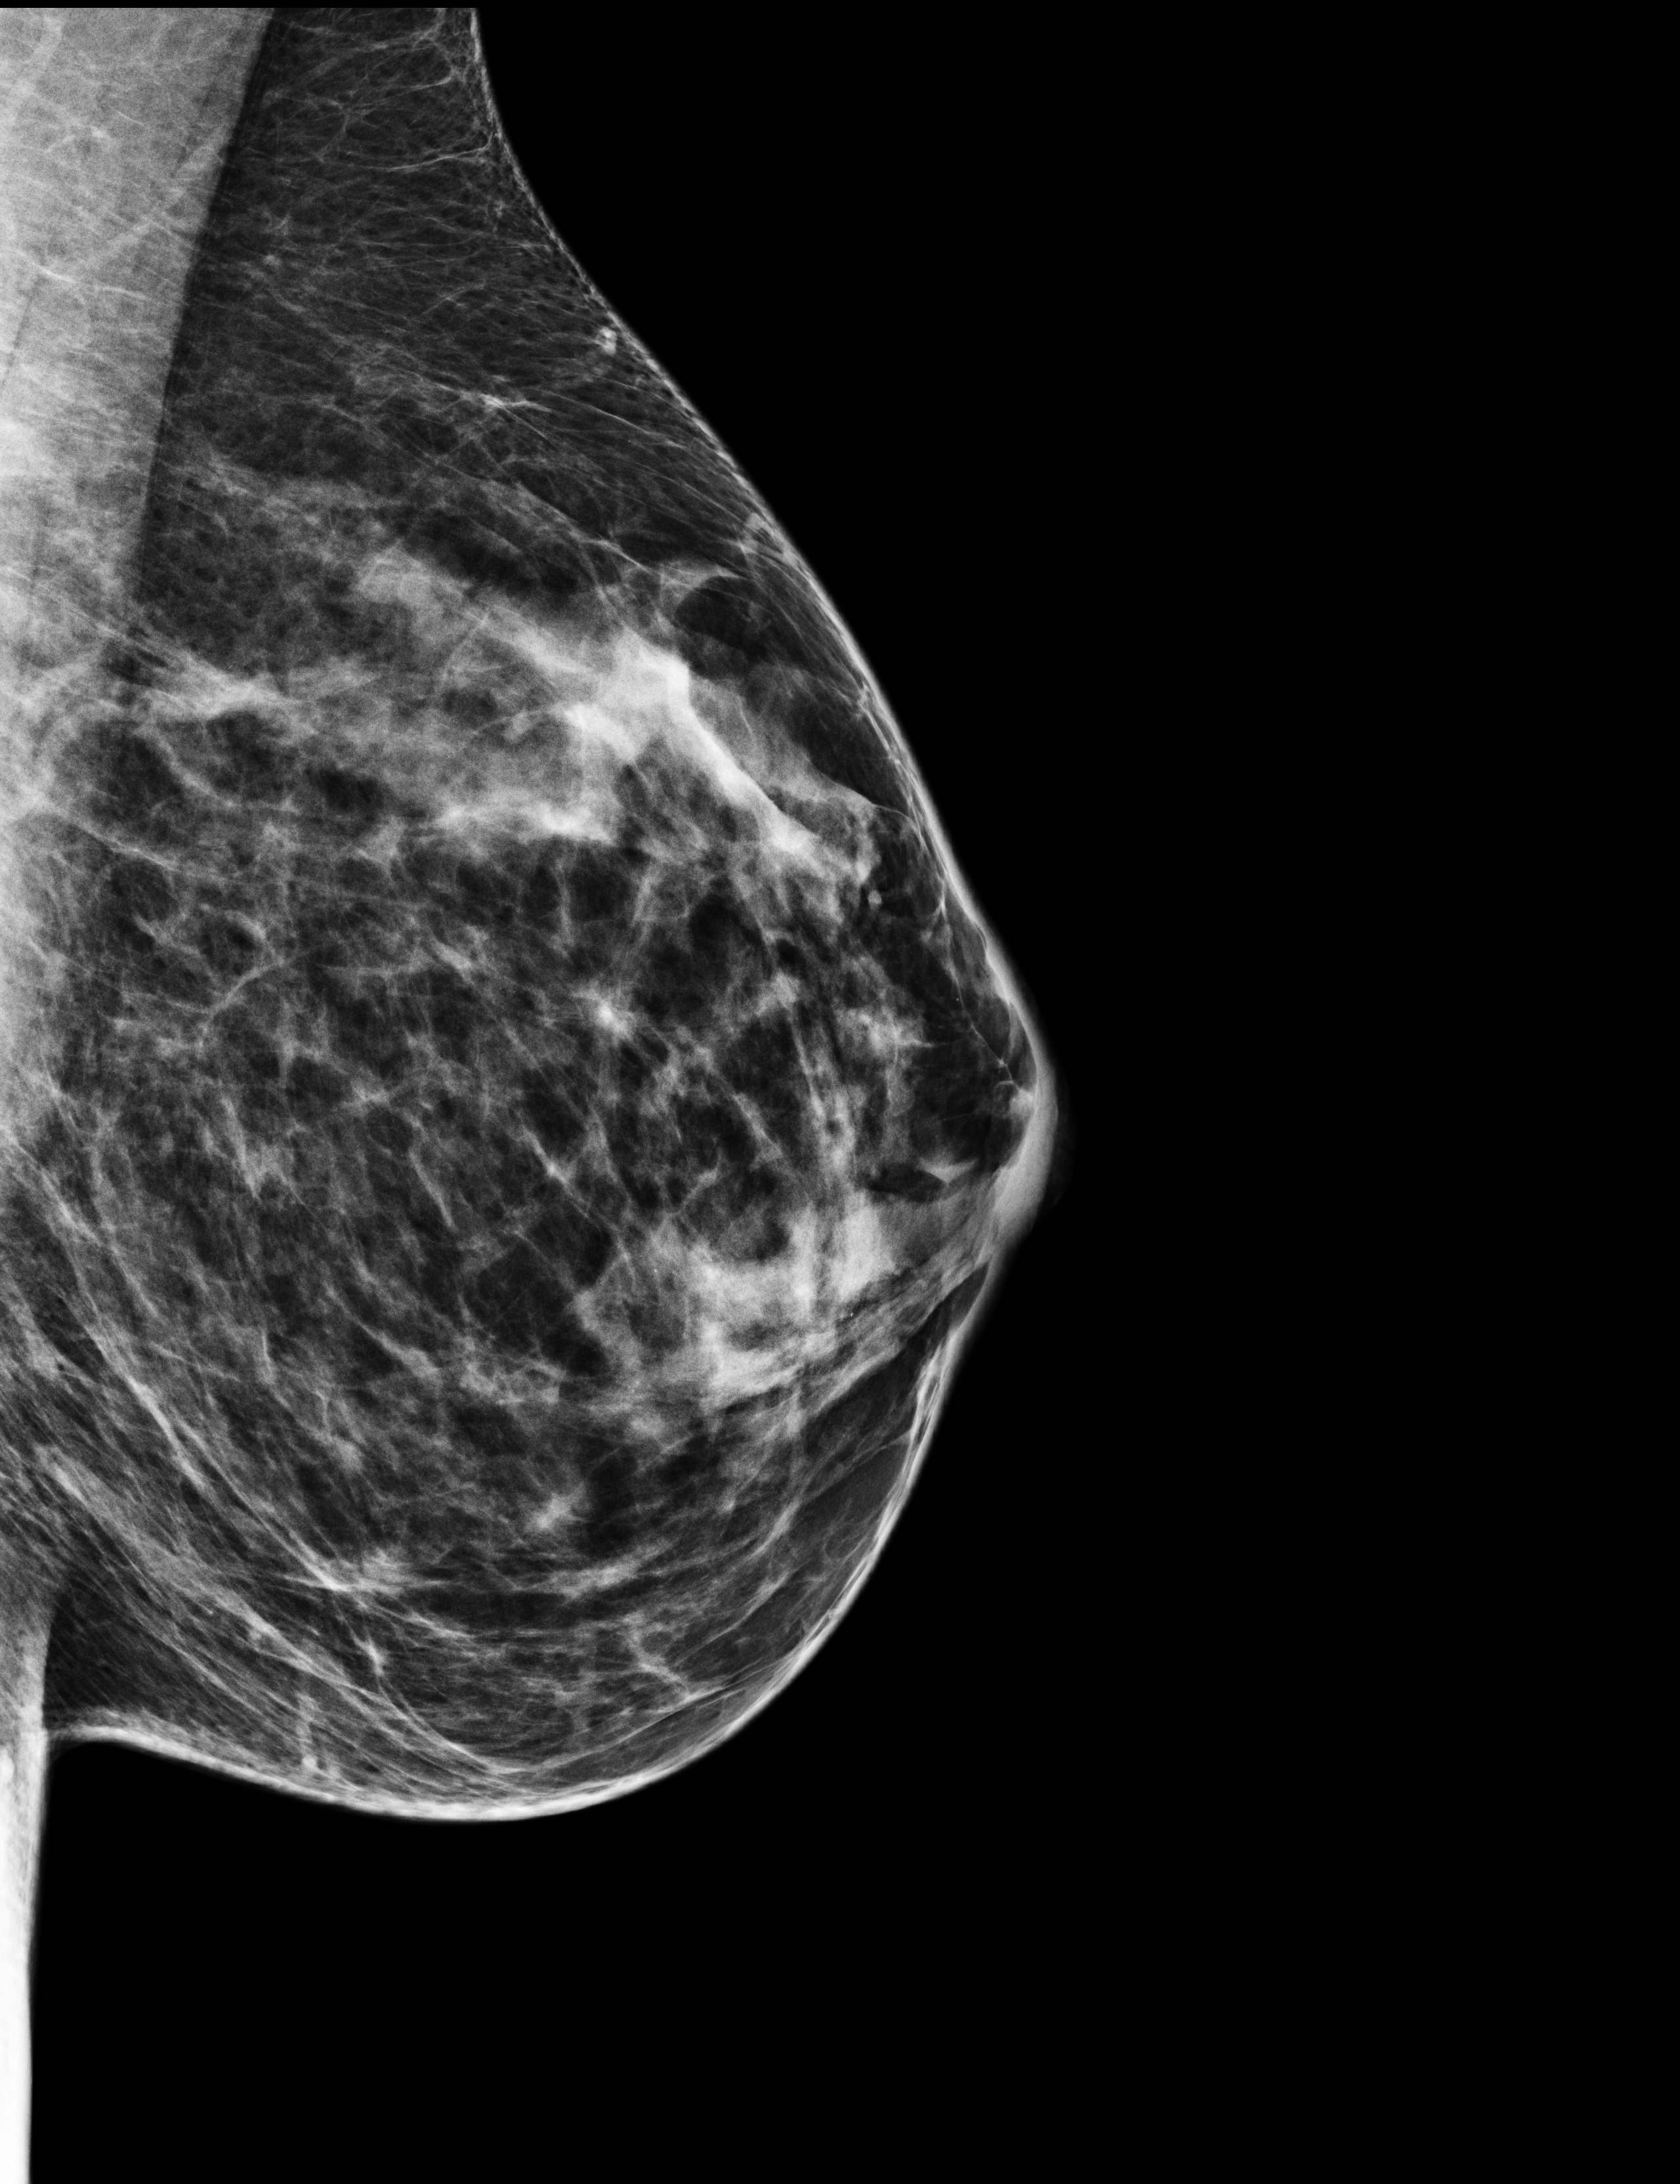
Annual screening mammography examination, compressed breast thickness 60 mm, system: Selenia Dimensions. Patient: female, 45 years.
Image type: full-field digital mammogram. Breast: left. Projection: MLO view.